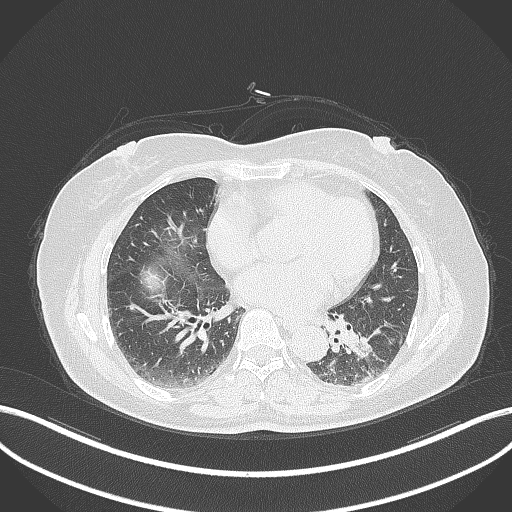
Chest CT, one axial slice; reconstruction kernel B70f; 120 kVp; lung window (W 1500 / L -600 HU); 1 mm slice thickness; 512 × 512 image matrix. Patient: female, 59 years. From the clinical record (not read from this slice): clinical TNM (as recorded): T2a N0 M0; histopathological grade: G2-3.
Annotated regions visible in this slice (rectangle marked by the reading radiologist):
- lung tumour (recorded histology: adenocarcinoma): bounding box <339,319,384,364> (left, top, right, bottom; pixels)